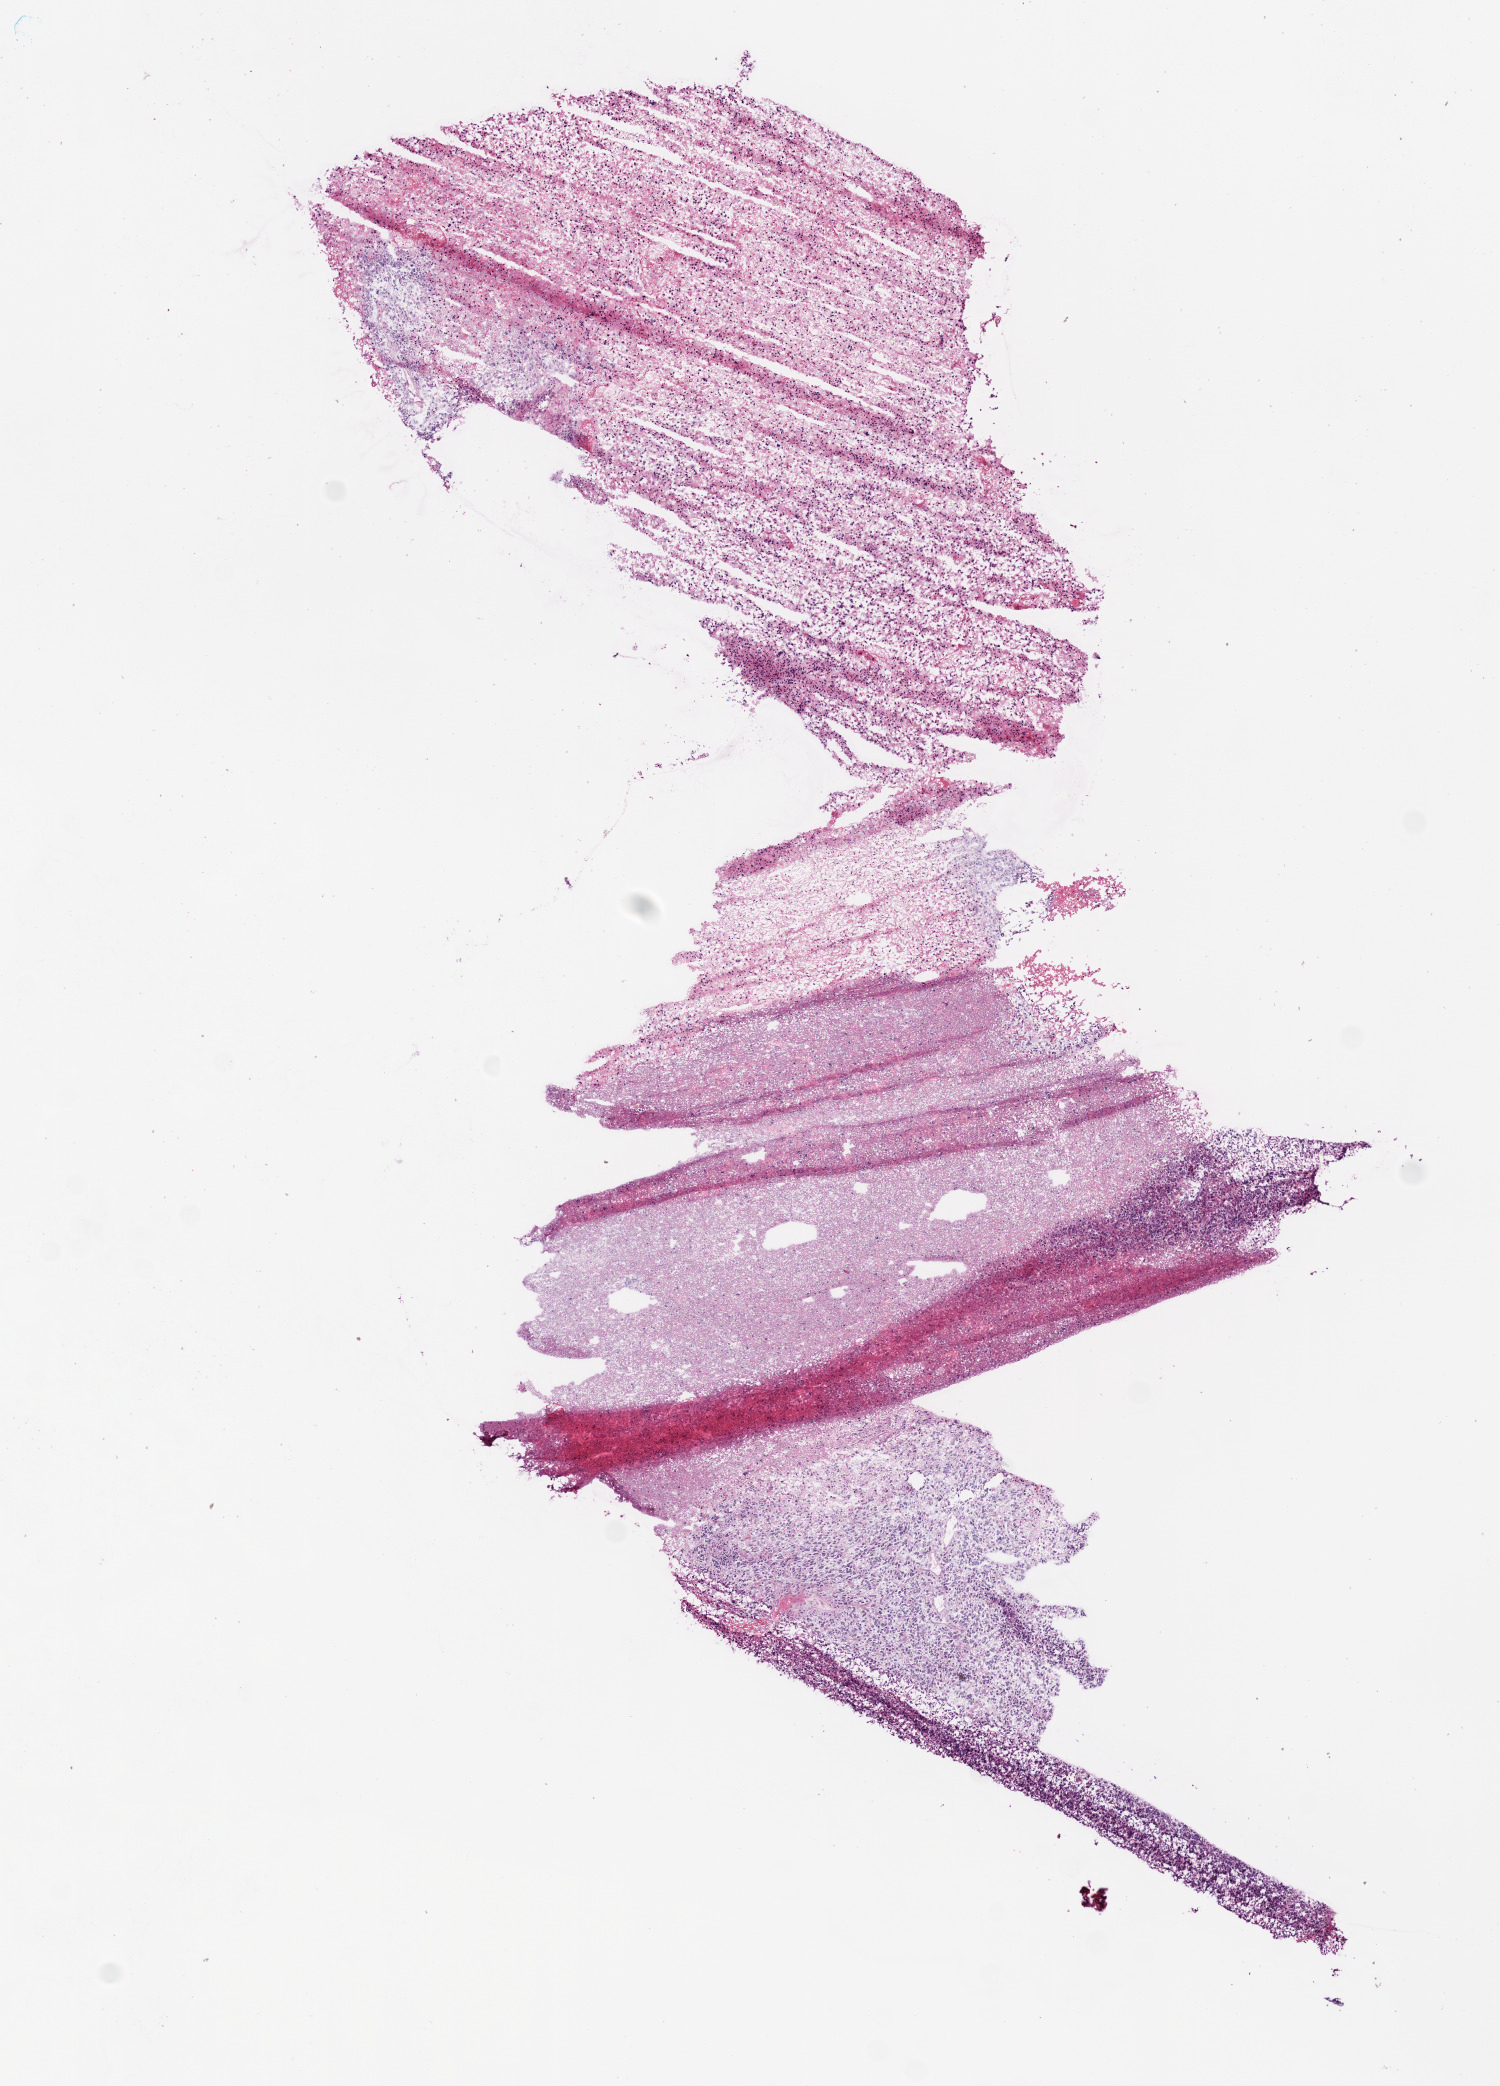
Digitized H&E-stained tissue section (whole slide), whole scanned area (about 6.0 x 8.4 mm, acquisition: 20x scan) shown as a low-resolution overview; frozen section from the bottom of the tissue portion; sample: primary tumour, brain. Male patient; age at initial diagnosis 21 years. Composition of this section per pathologist review: tumour cells 40%, tumour nuclei 95%, normal cells 20%, stromal cells 0%, necrosis 40%.
Histologic diagnosis: Glioblastoma.